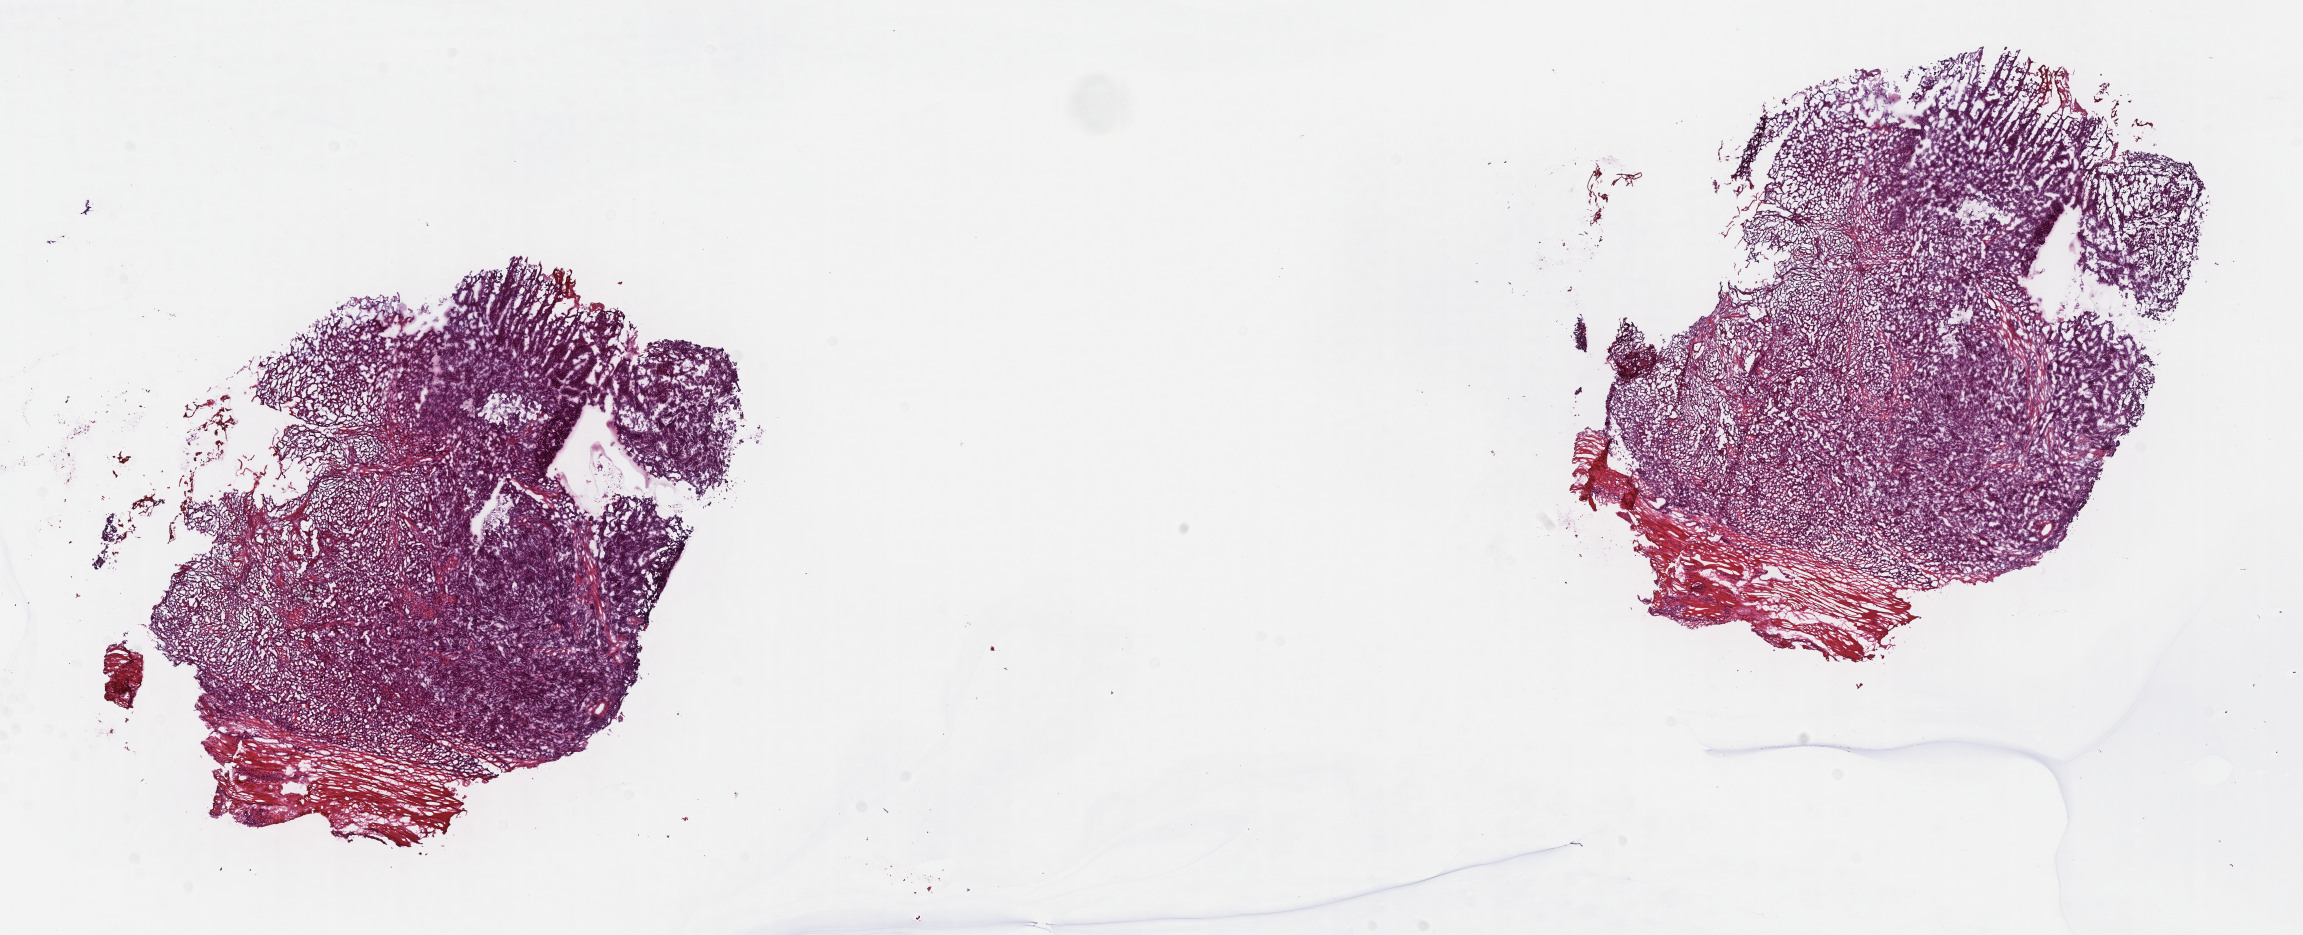
Whole-slide histology image, H&E-stained, a low-resolution overview of the entire scanned area, about 18.6 x 7.6 mm (from a 40x scan); frozen section from the top of the tissue portion; sample: primary tumour, mesothelium. Male patient; age at initial diagnosis 62 years. Slide review estimates, as recorded: tumour cells 80%, tumour nuclei 80%, normal cells 0%, stromal cells 20%, necrosis 0%. Infiltration values recorded for this section: lymphocyte infiltration 70%, monocyte infiltration 10%, neutrophil infiltration 10%.
• AJCC pathologic stage: III (7th edition)
• laterality: right
• pathologic diagnosis: Epithelioid mesothelioma, malignant (lung, NOS)